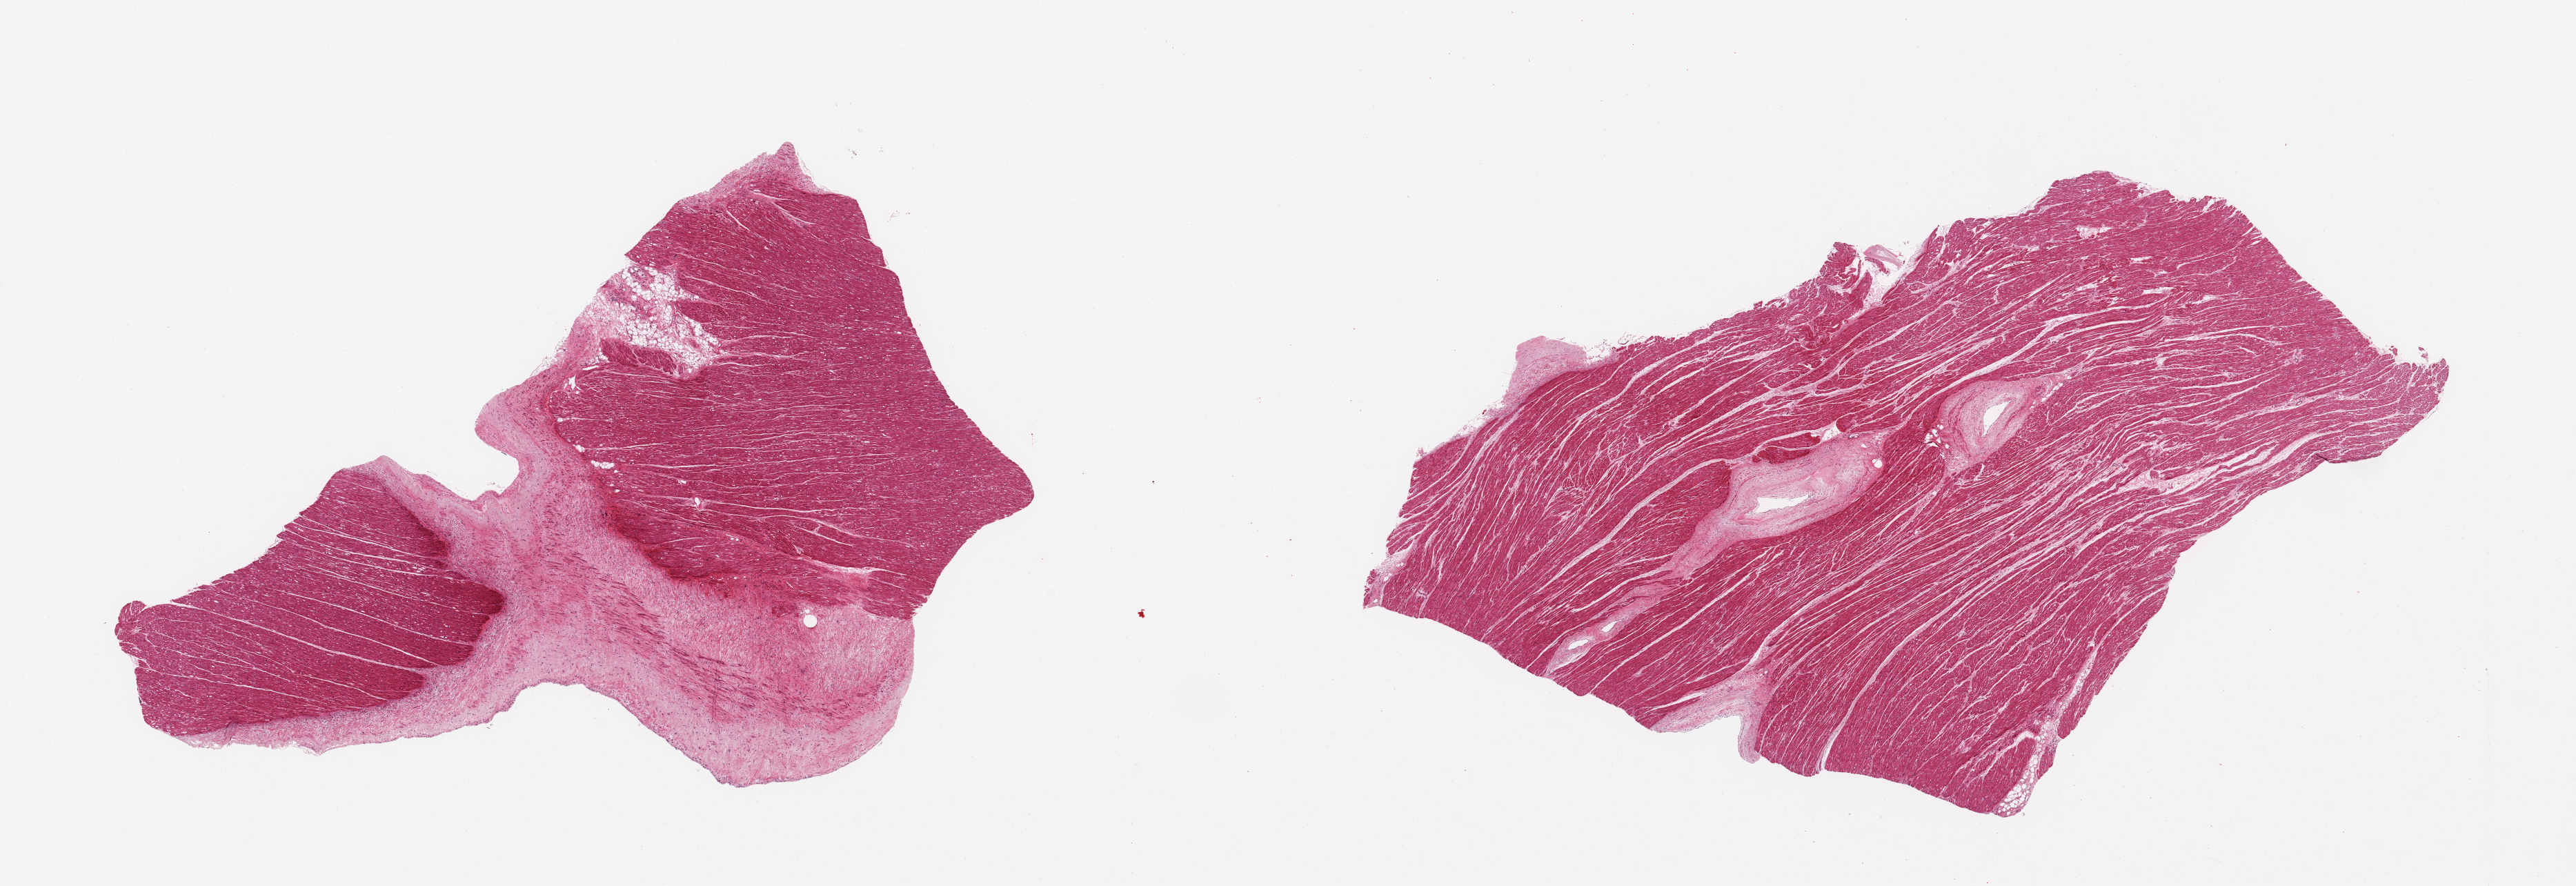
Digitized haematoxylin and eosin-stained section, brightfield, whole scanned area (about 29.5 x 10.2 mm, from a 20x scan) shown as a low-resolution overview; PAXgene-fixed, paraffin-embedded tissue; target tissue: auricular appendage; tissue donor sample. Donor: male.
Pathologist's review note for this sample: 2 pieces; one consists of myocardium and ~30-40% fibrous tissue with focal fat; other consists of myocardium and intramuscular vessles.